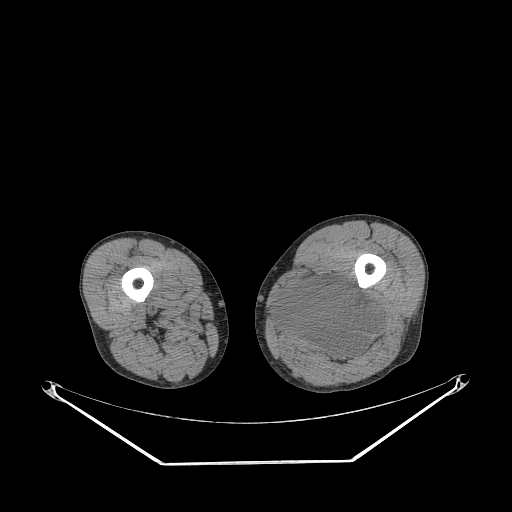
CT of an extremity soft-tissue mass (from a PET/CT study), one axial slice. Position 231 of 267 along the scan axis. Soft-tissue window (W 400 / L 40 HU). 512 × 512 image matrix, field of view 500 × 500 mm. Male patient. From the clinical record (not read from this slice): histological type: undifferentiated pleomorphic liposarcoma; grade: high; site of the primary tumour: left thigh.
Outlined on this slice (expert contour drawn on MRI and transferred to this co-registered scan by the dataset authors):
- gross tumour volume including surrounding oedema: bounding box (x1, y1, x2, y2) in pixels: (274, 278, 380, 362)
- gross tumour volume (mass): (276, 278, 380, 362)